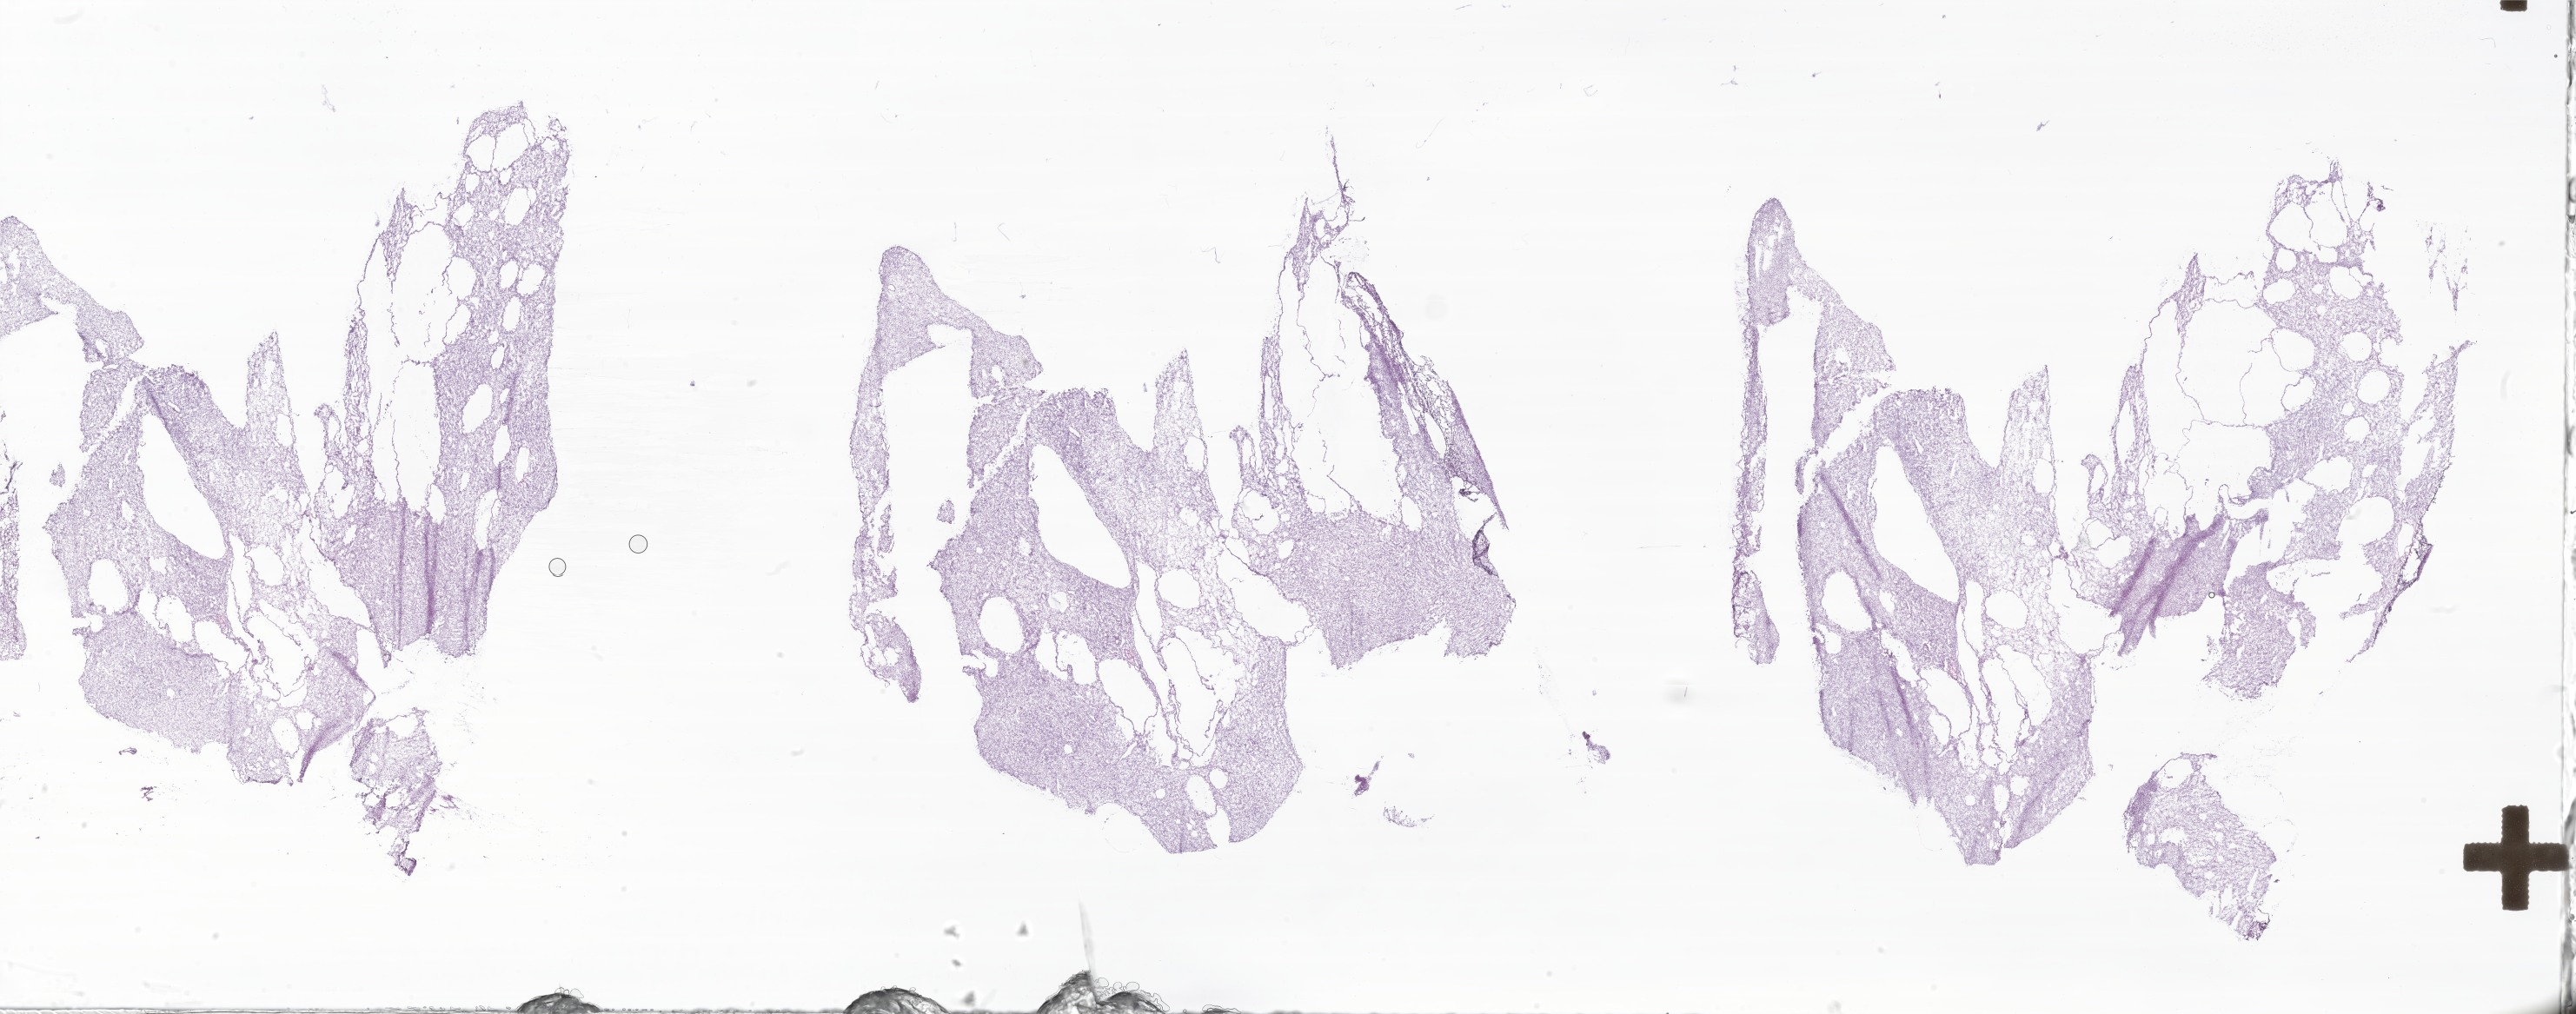
Haematoxylin and eosin whole-slide image of tumor tissue from the kidney, low-resolution overview of the scanned area, about 50.0 x 19.7 mm; cryosection (OCT / tissue freezing medium). Patient male; age 572 days (about 1.6 years).
• diagnosis (ICD-O-3 morphology term): Clear cell sarcoma of kidney